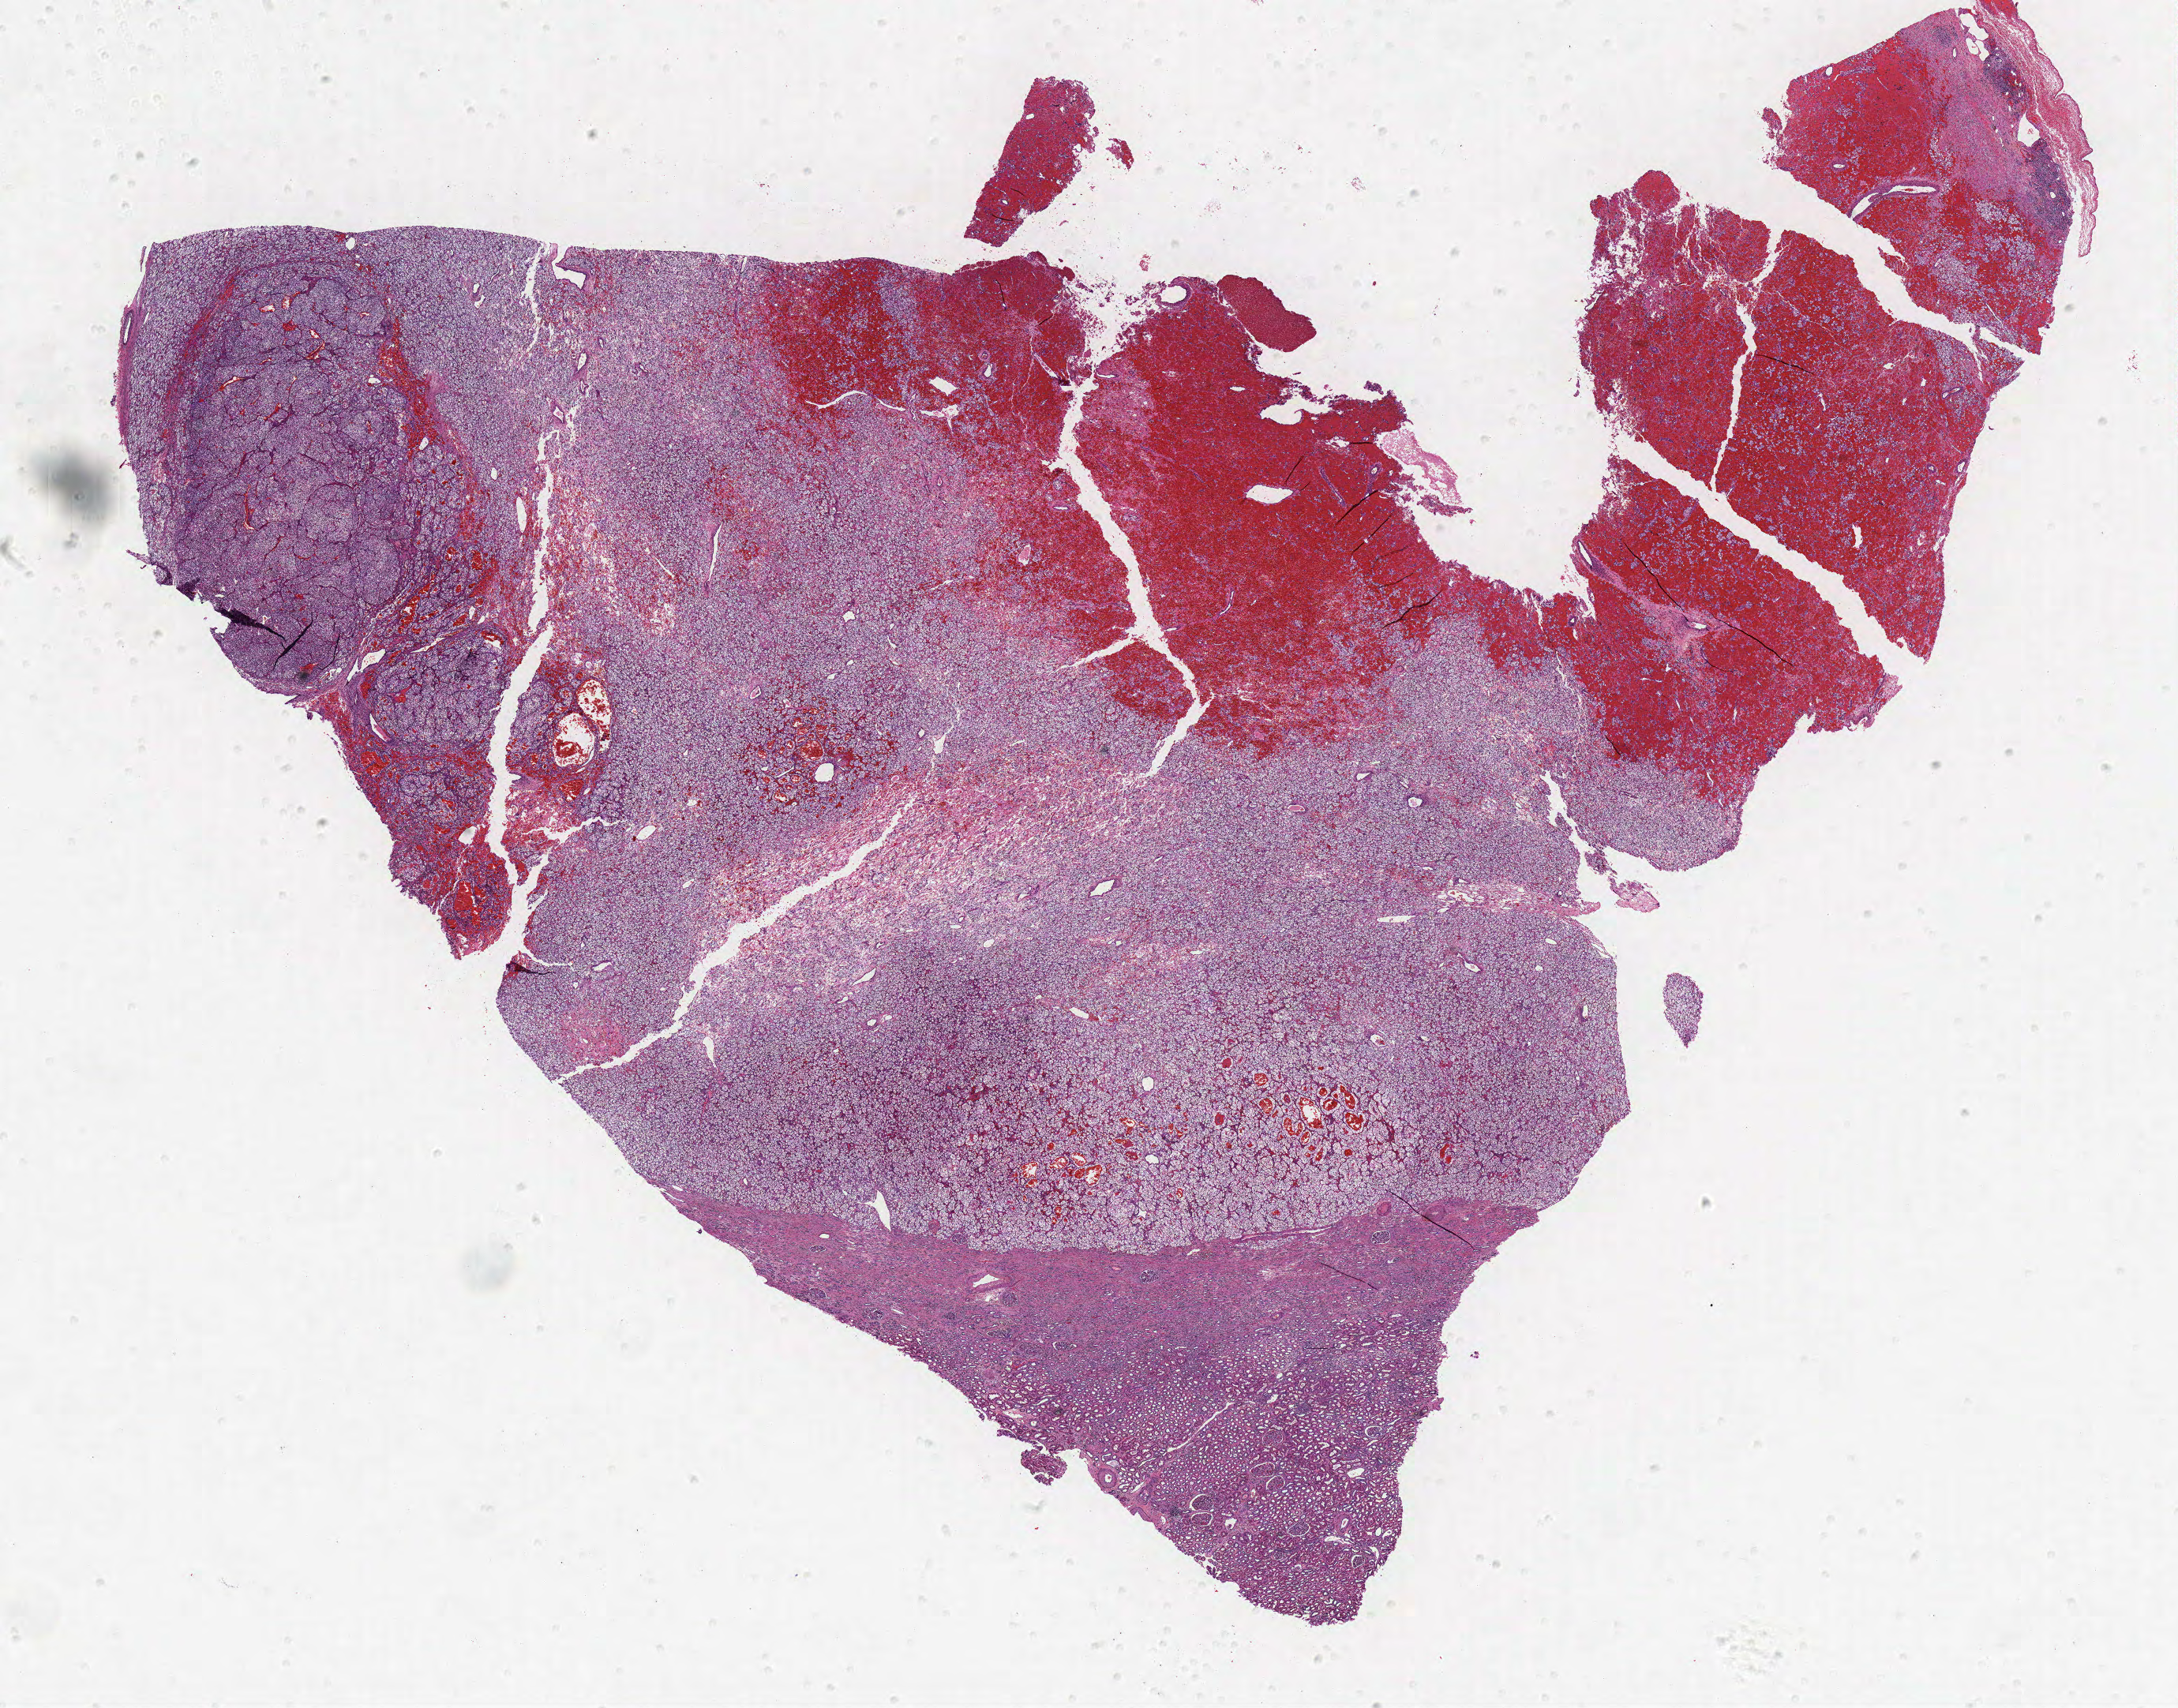
Digitized H&E-stained tissue section (whole slide), a low-resolution overview of the entire scanned area, about 22.1 x 17.3 mm (acquisition: 40x scan), formalin-fixed paraffin-embedded (FFPE) diagnostic section, sample: primary tumour, kidney. Male patient; age at initial diagnosis 54 years. Histologic grade: G3 (poorly differentiated).
AJCC pathologic stage: I. Laterality: left. Diagnosis: Clear cell adenocarcinoma, NOS.